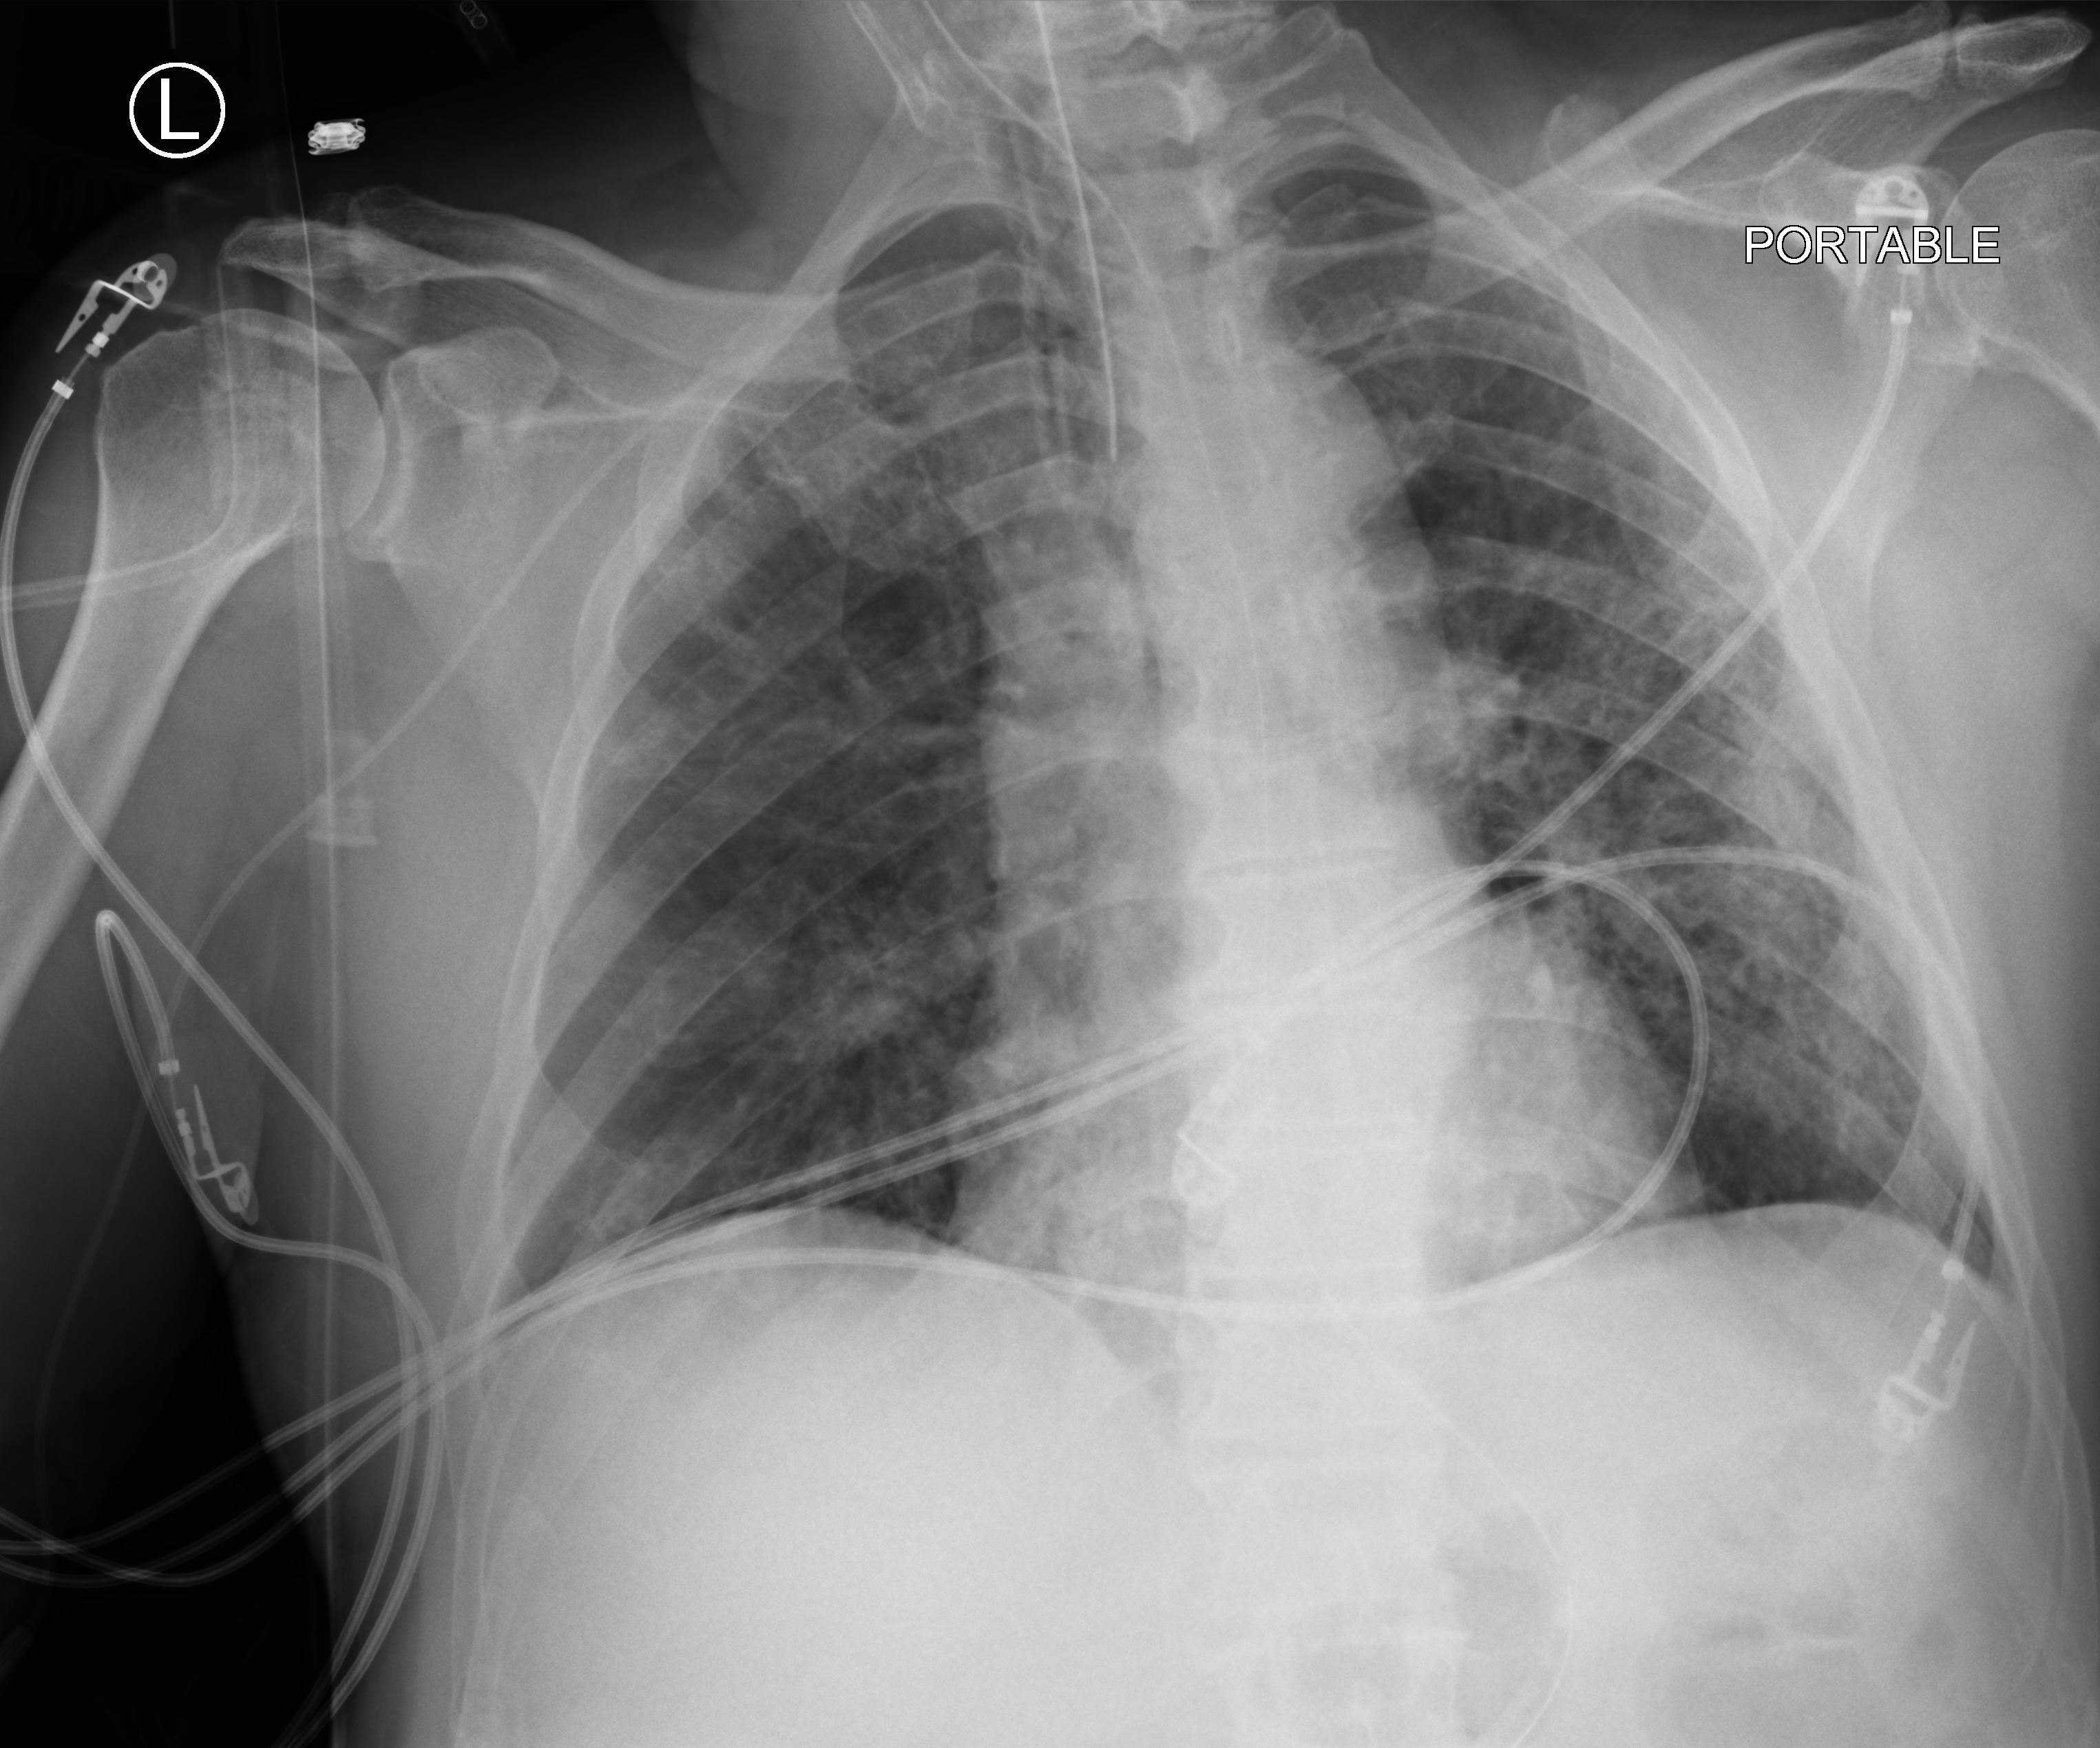
Chest X-ray (portable). Patient hospitalised with COVID-19; male, aged 60–74 years.
Admission-level facts for this patient (not findings on this image; timing relative to this image not recorded):
- admitted to intensive care during this hospital stay: yes
- length of hospital stay: 20 days